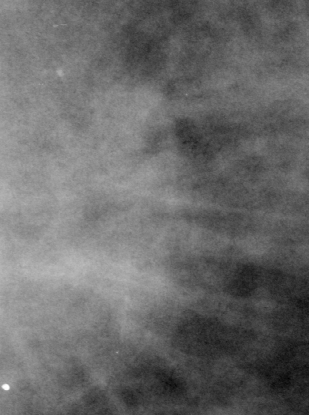
Crop from a digitized film mammogram around one marked abnormality; left breast; CC view.
Marked abnormality: mass, shape irregular, margins spiculated; BI-RADS assessment category 5; subtlety rating 5 on a 1 (subtle) to 5 (obvious) scale; pathology result (as recorded, not read from the image): malignant.